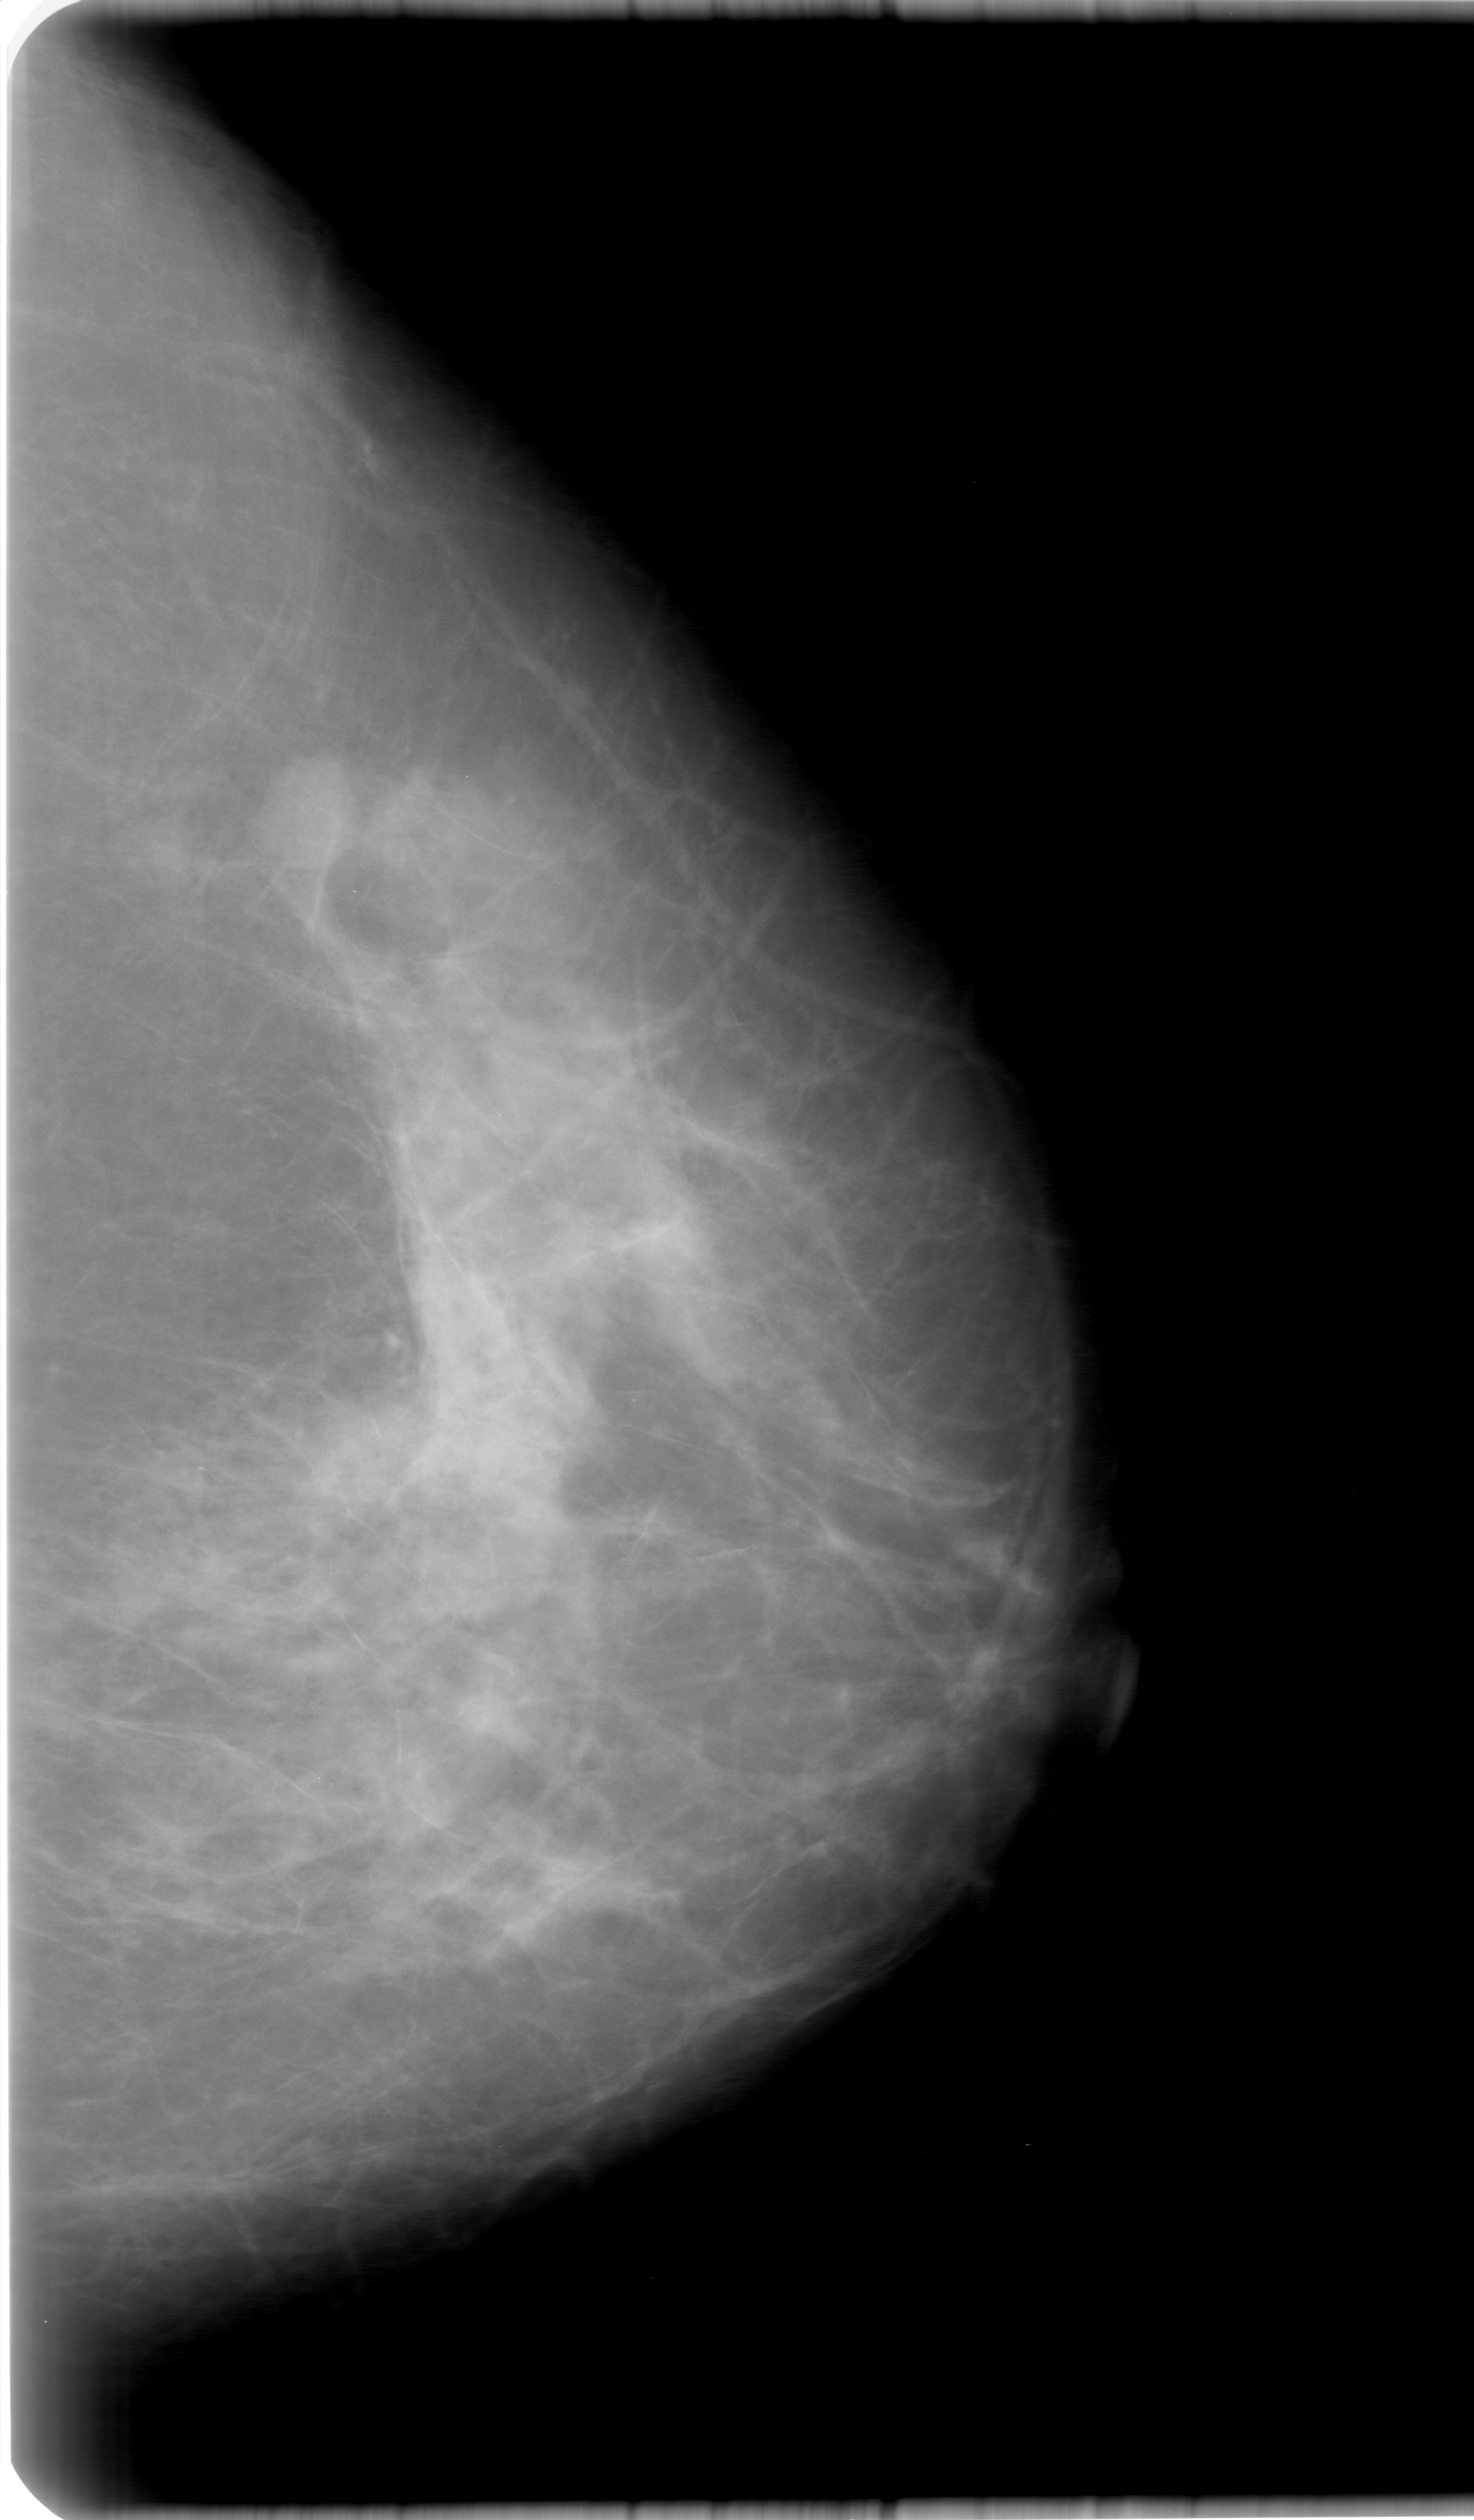
Digitized screen-film mammogram, left breast, craniocaudal (CC) view, BI-RADS breast density category 2 (scale 1–4).
Abnormality record for this image: mass, shape oval, margins microlobulated; BI-RADS assessment category 0 (incomplete: needs additional imaging); pathology (as recorded): benign.